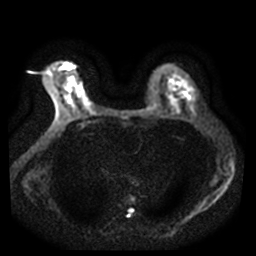
Breast MRI, one axial slice; slice 23 of 42 in the series (ordered by position); diffusion-weighted series; image 2 of 4 stored at this slice position (different b-values; order by instance number); 3 T; 5 mm slice thickness; 256 × 256 image matrix. Female patient.
Structures marked on this image (outlined manually by an expert reader):
- tumour on diffusion-weighted imaging: bounding box (x1, y1, x2, y2) in pixels: (64, 65, 69, 69)